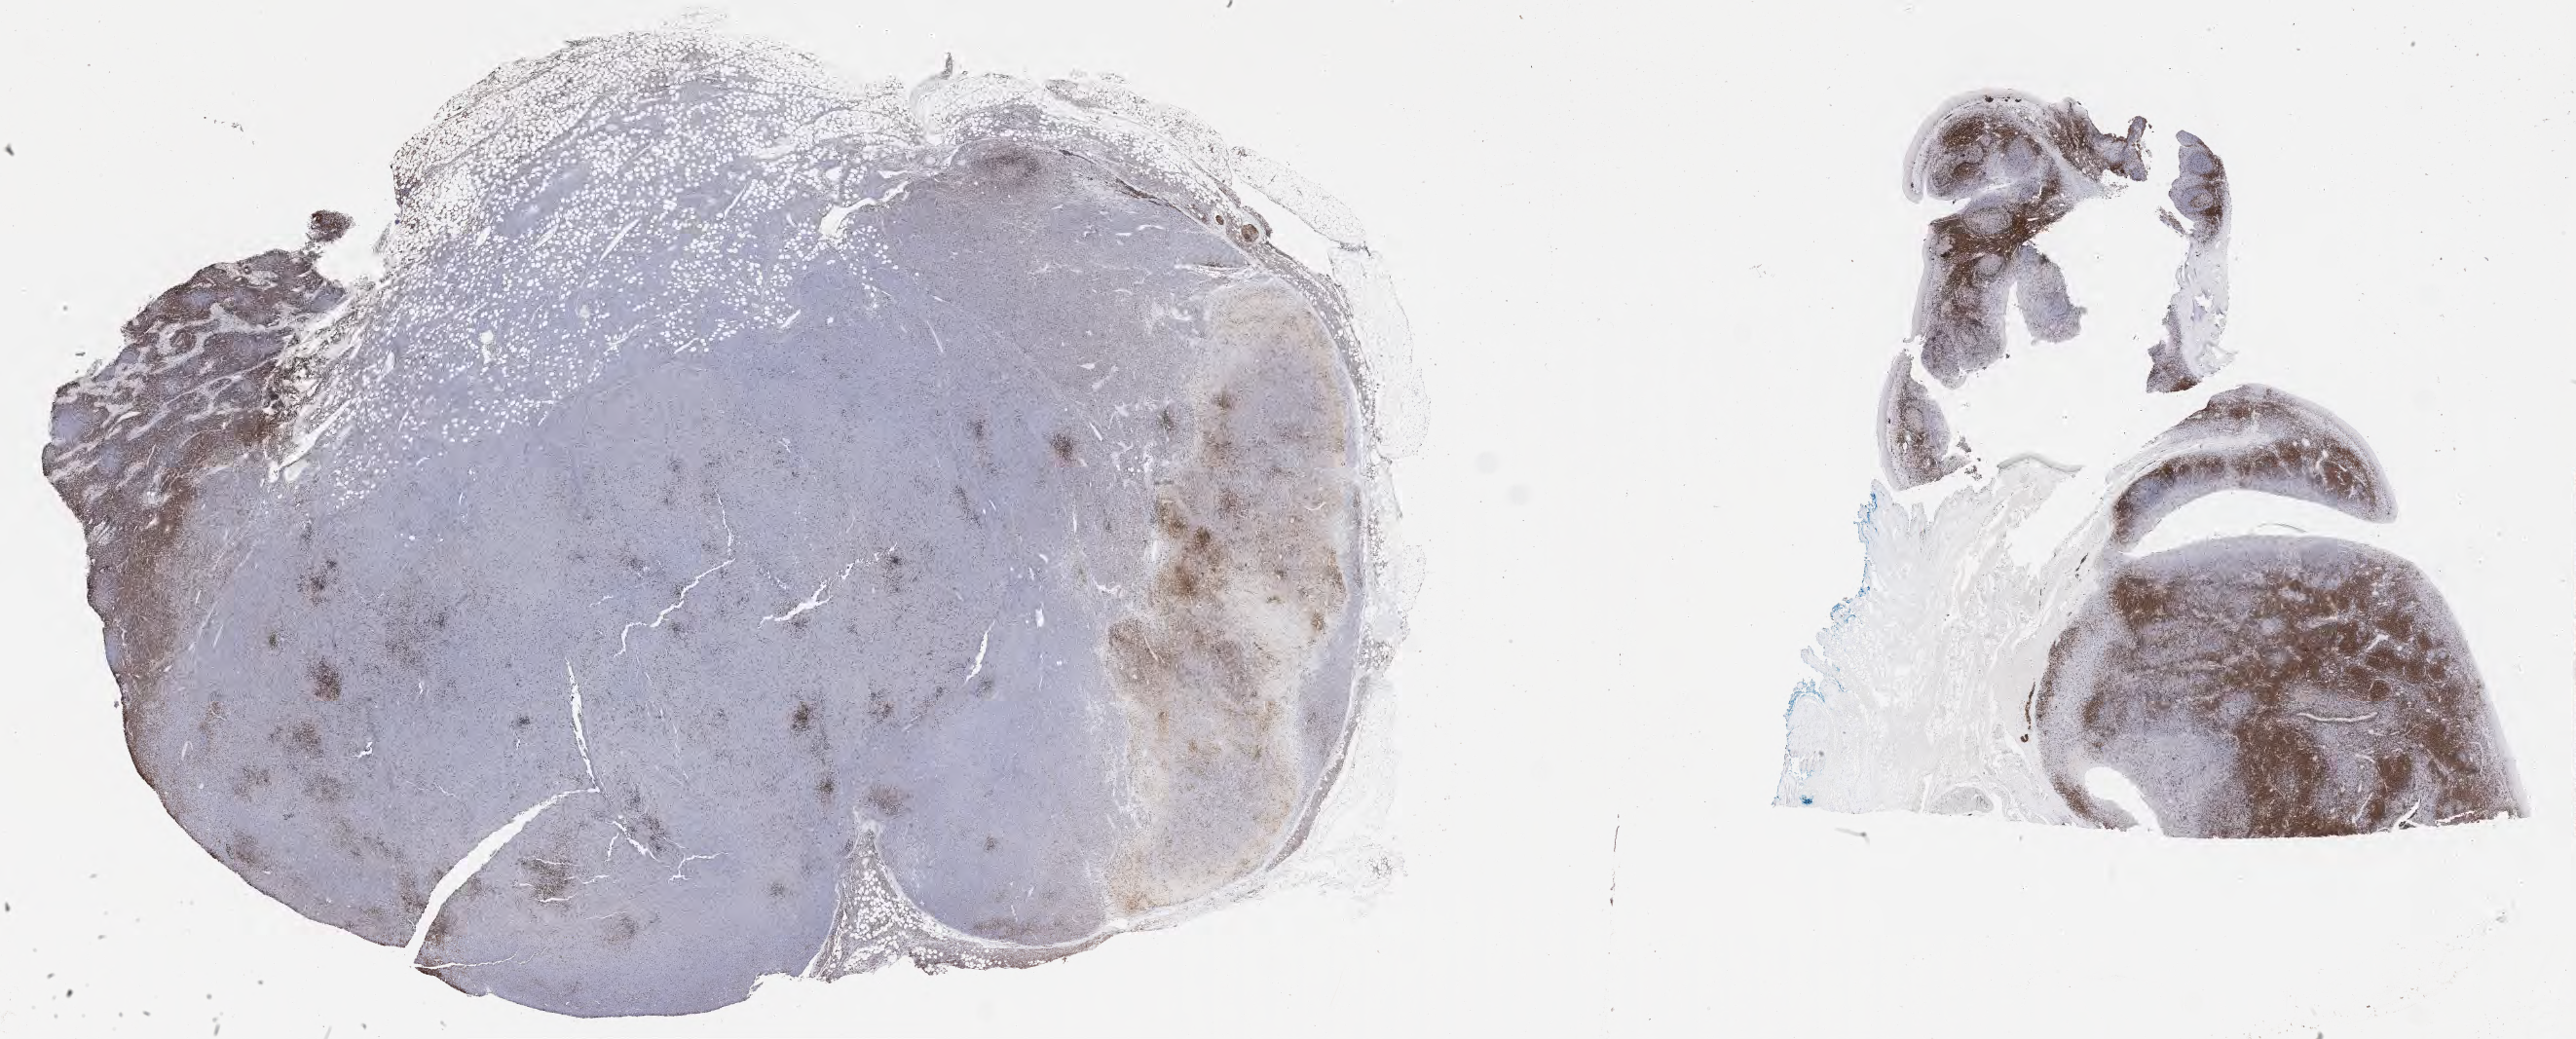
Whole-slide image, immunohistochemical stain for CD3, low-resolution overview of the scanned area, about 42.8 x 17.3 mm. Tumor tissue. Male patient, aged 57.
• diagnosis: Burkitt lymphoma, NOS